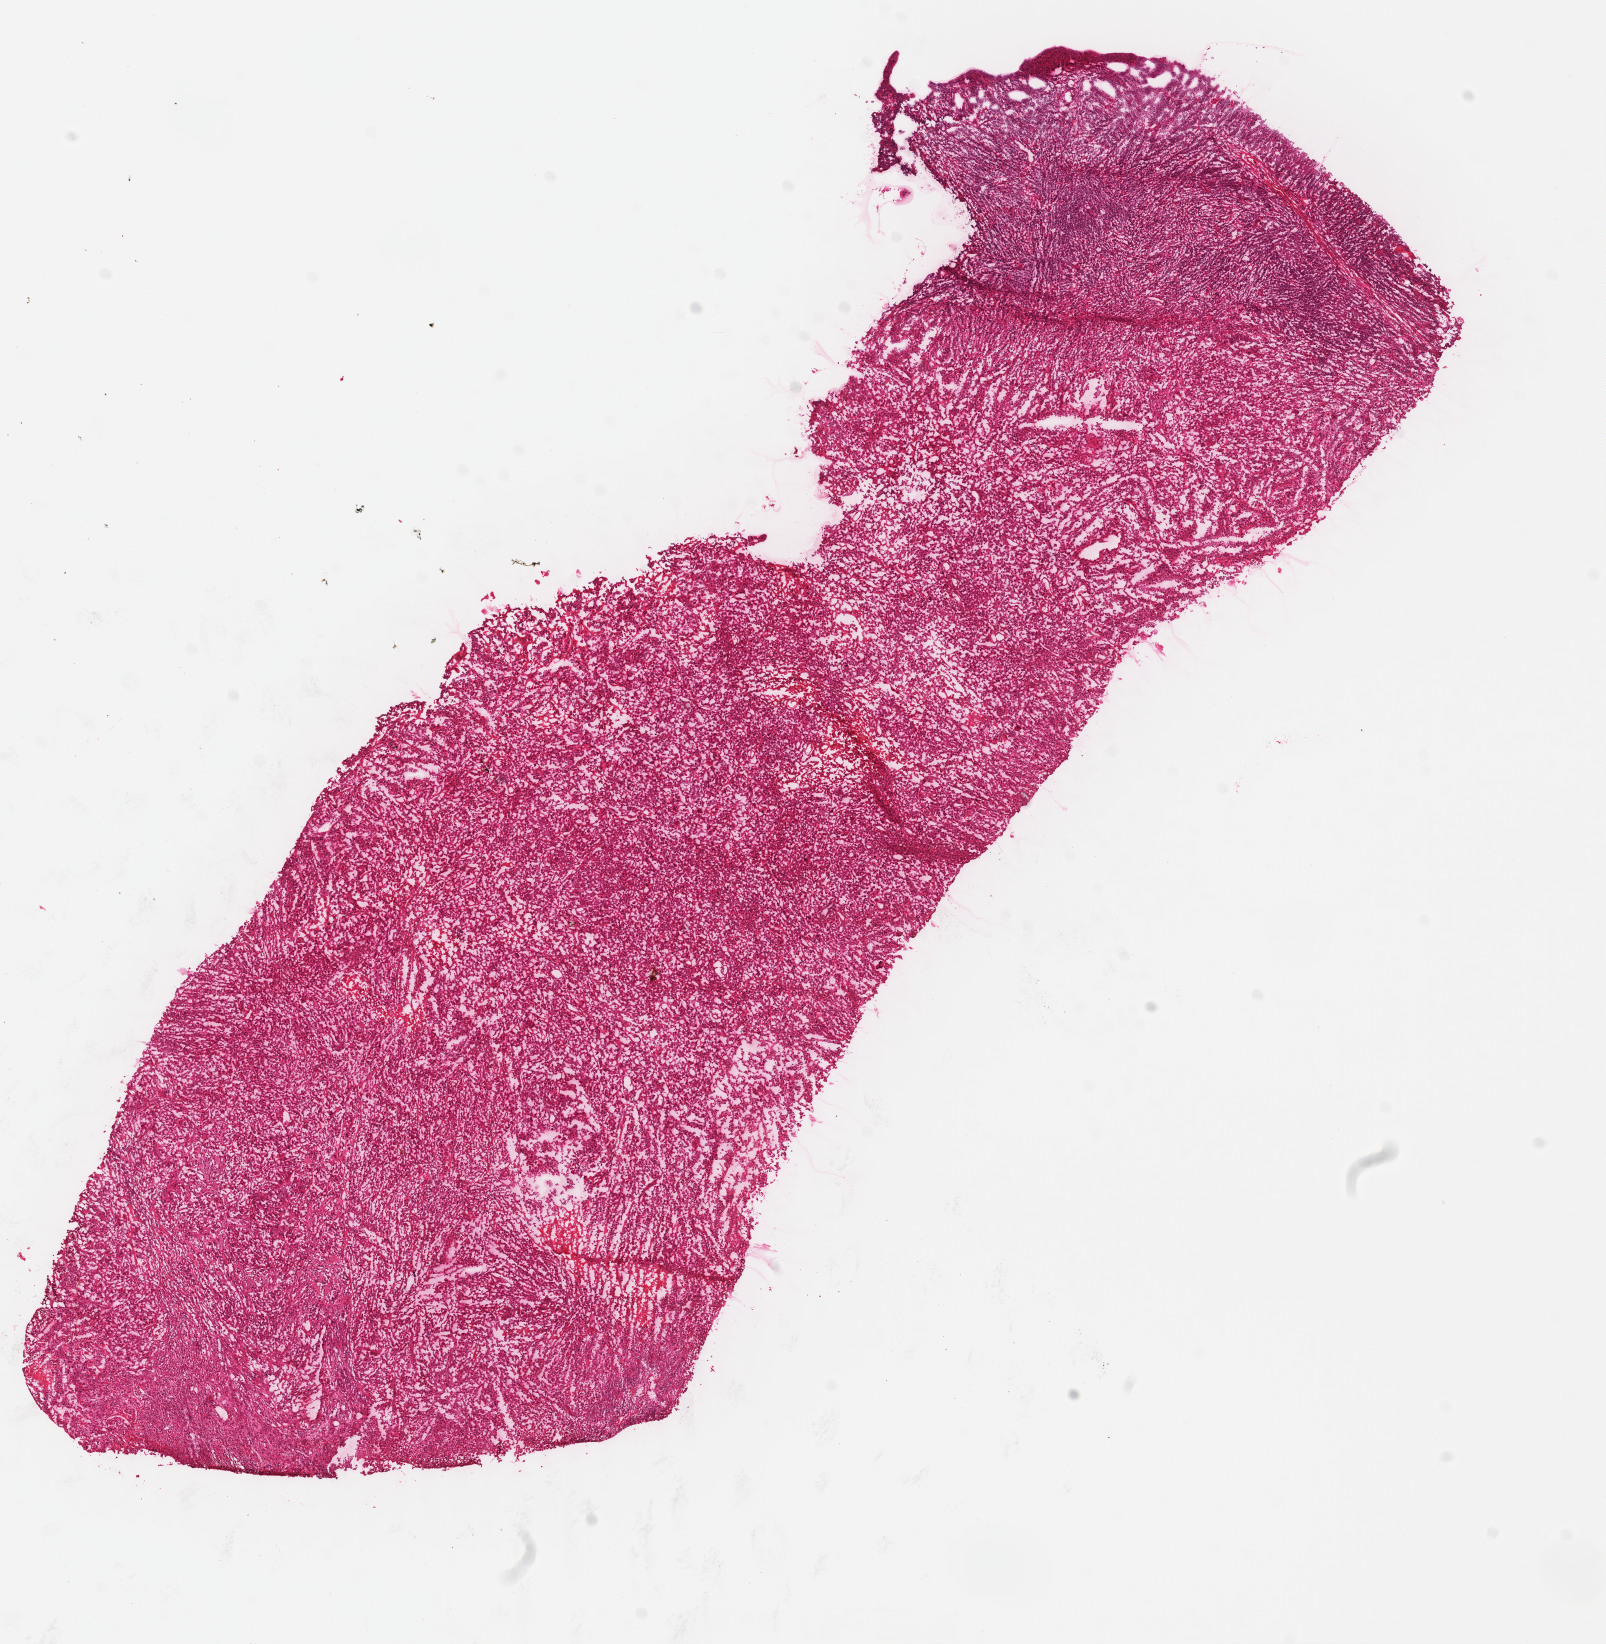
Hematoxylin and eosin (H&E) stained whole-slide image, whole scanned area (about 12.6 x 12.9 mm, slide scanned at 40x) shown as a low-resolution overview. Formalin-fixed paraffin-embedded (FFPE) diagnostic section. Sample: primary tumour, skin. Patient: male, age at initial diagnosis 70 years.
Diagnosis: Malignant melanoma, NOS. AJCC pathologic stage: III.